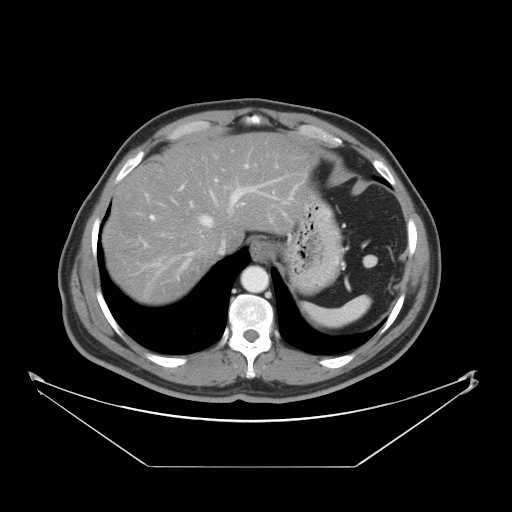
Contrast-enhanced abdominal CT, one axial slice. Slice 36 of 46 in the series (ordered by position). Intravenous contrast given. Soft-tissue window (W 400 / L 40 HU). 512 × 512 image matrix, field of view 465 × 465 mm. Male patient, age 57 years. Case-level facts recorded for this patient, not image findings: diagnosis: colorectal cancer liver metastases, imaged before liver resection; multiple liver metastases: no.
Structures marked on this image (manually delineated by an expert):
- hepatic veins: box from (x=186, y=178) to (x=281, y=256) px
- liver: (x=105, y=136)–(x=310, y=305)
- planned liver remnant (the part of the liver to remain after resection): (x=105, y=136)–(x=310, y=301)
- portal vein (with intrahepatic branches): (x=140, y=164)–(x=248, y=280)